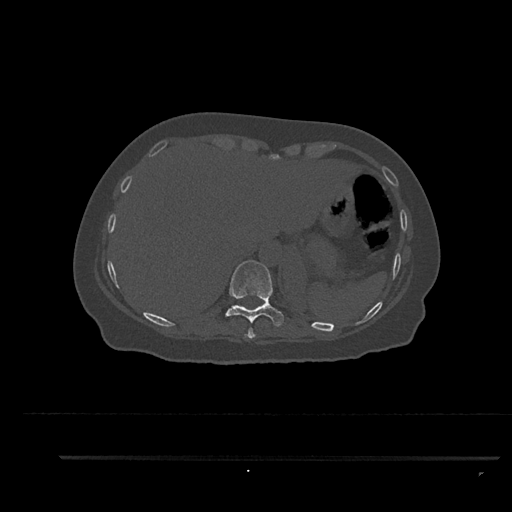
CT including the spine, one axial slice. Position 365 of 797 along the scan axis. Reconstruction kernel Br40s/3. Bone window (W 1800 / L 400 HU). 512 × 512 image matrix, field of view 408 × 408 mm. Patient: female, 44 years. From the clinical record (not read from this slice): primary cancer: renal; vertebrae with lytic lesions (as recorded): L1.
Structures marked on this image (semi-automatic segmentation, software-assisted and operator-edited):
- T10 vertebra: bounding box (x1, y1, x2, y2) in pixels: (225, 260, 284, 331)
- T9 vertebra: (244, 328, 256, 339)